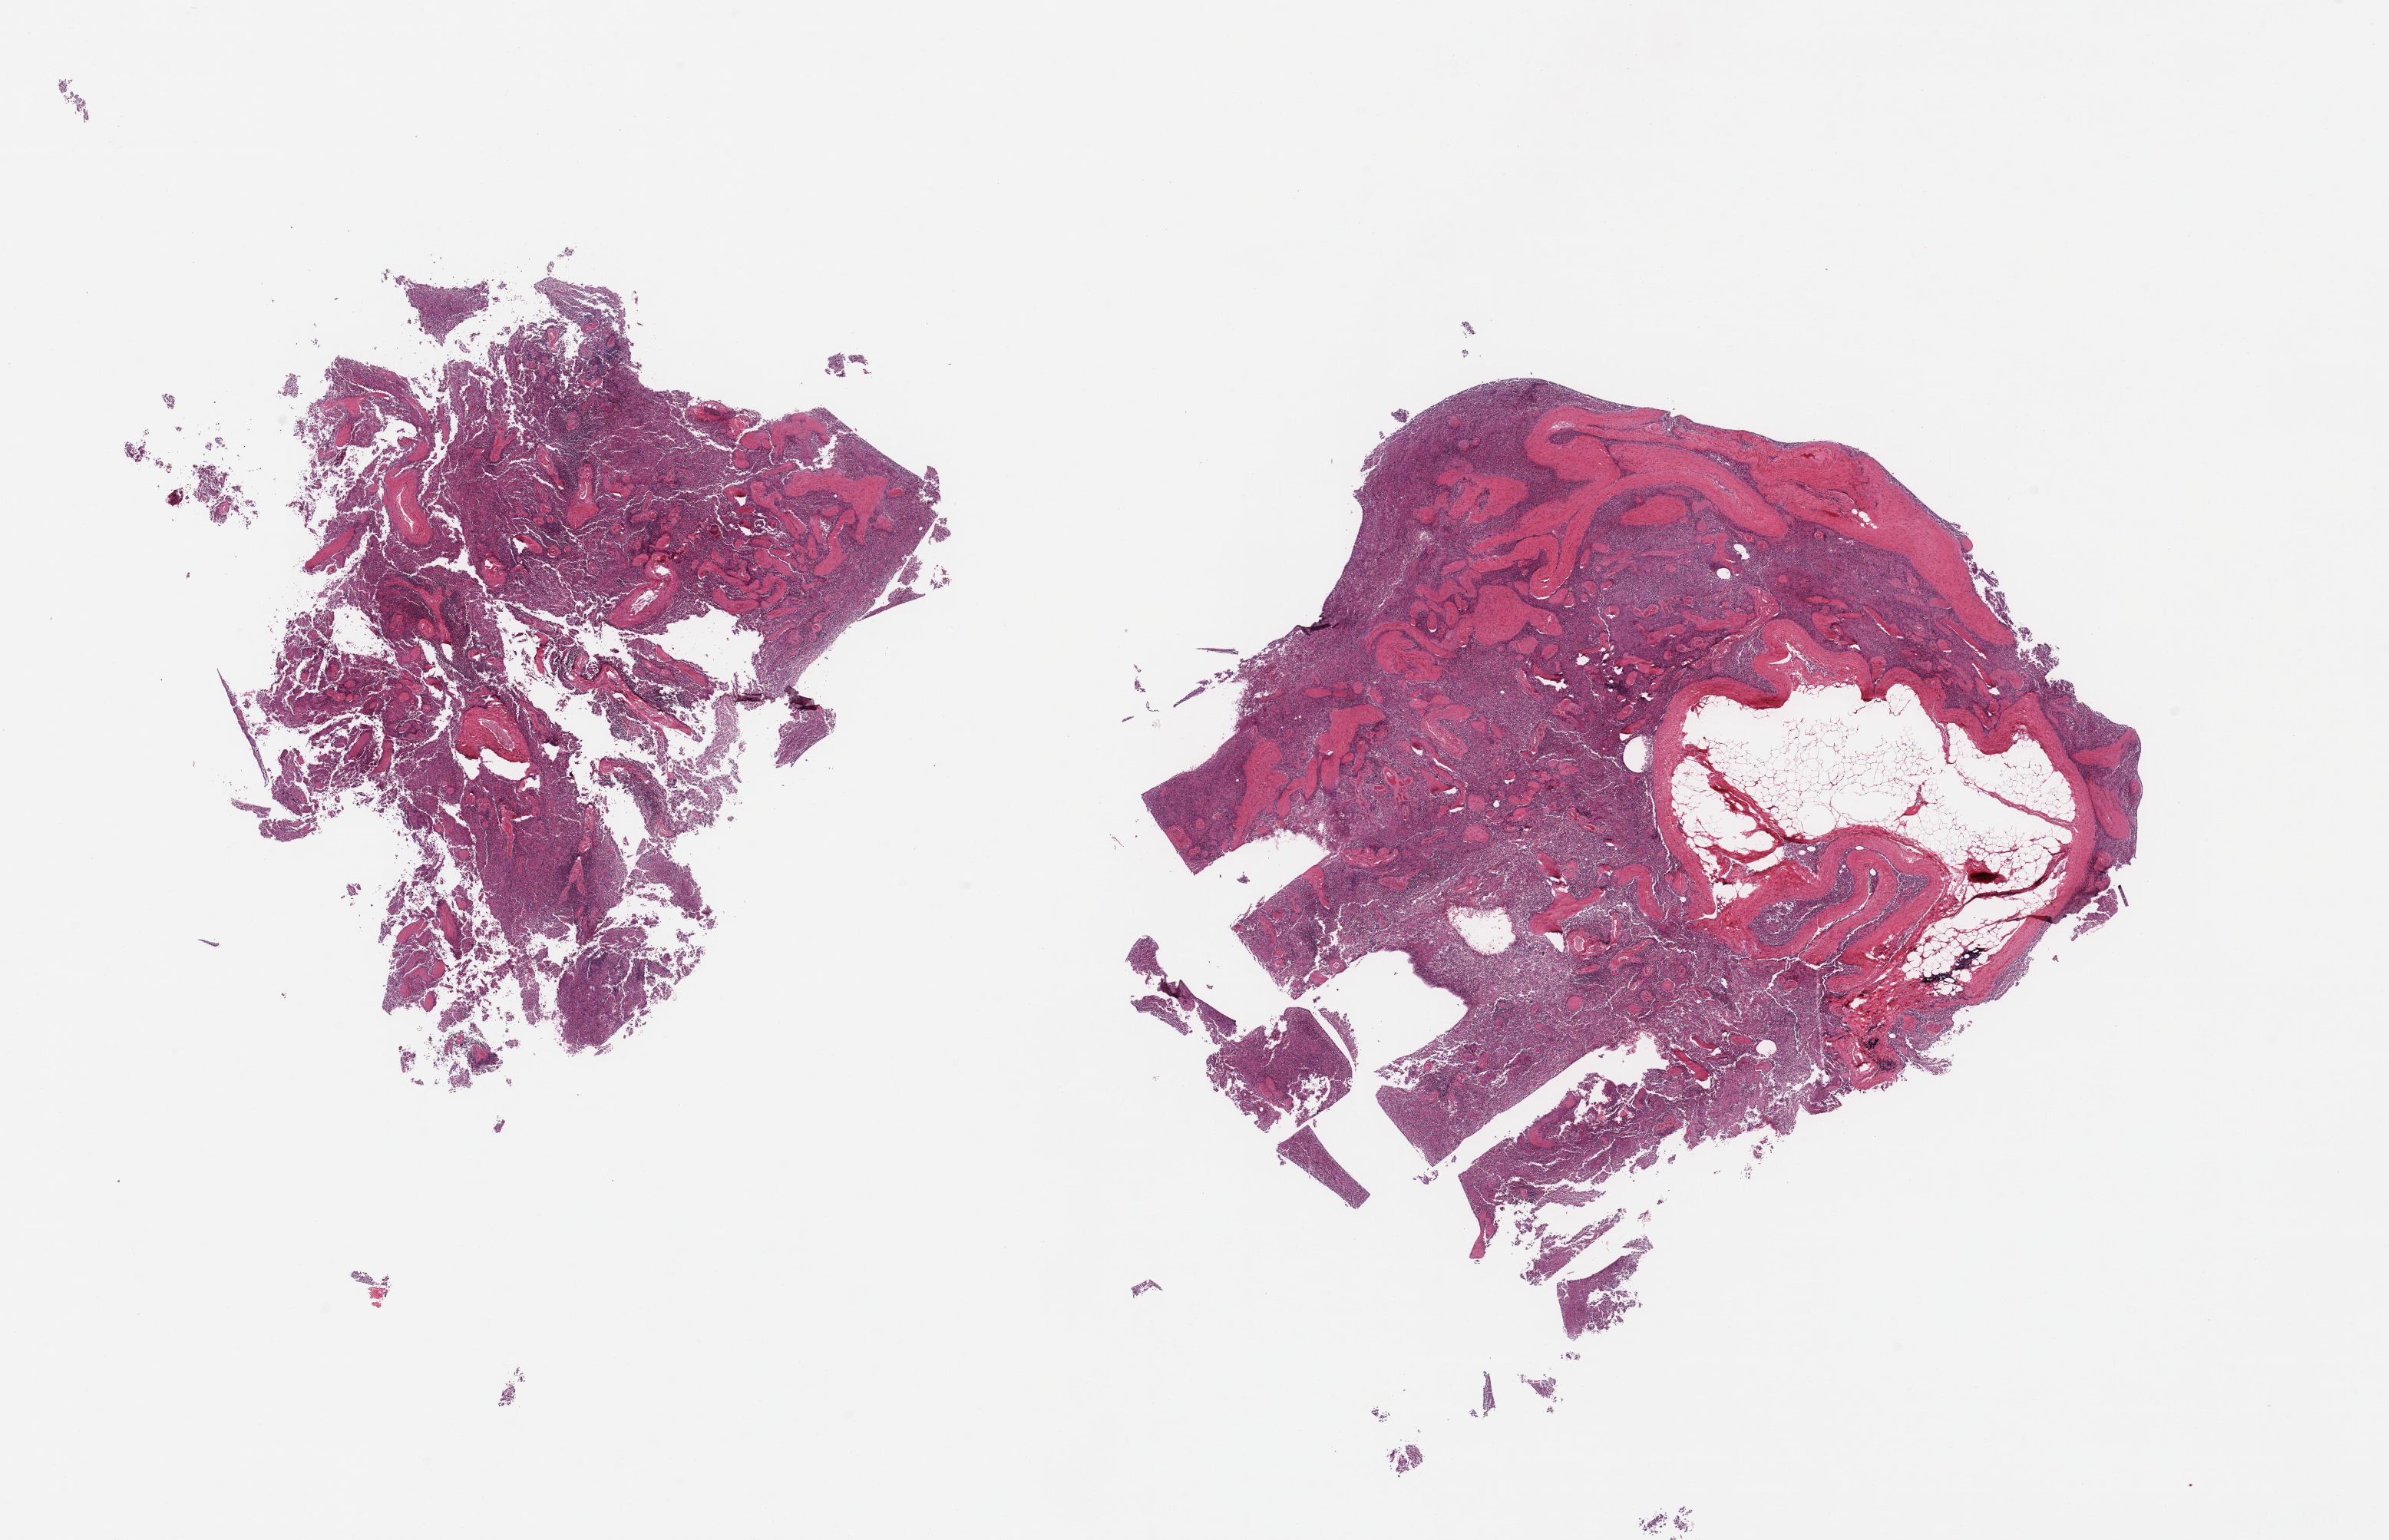
Haematoxylin and eosin whole-slide image, shown as a low-resolution overview of the whole scanned area (about 24.6 x 15.9 mm); PAXgene-fixed, paraffin-embedded tissue; sampled site (target tissue): spleen; donor tissue sample.
Review note (as recorded): 2 pieces; significant component is vessels/trabeculae, portion of fat.